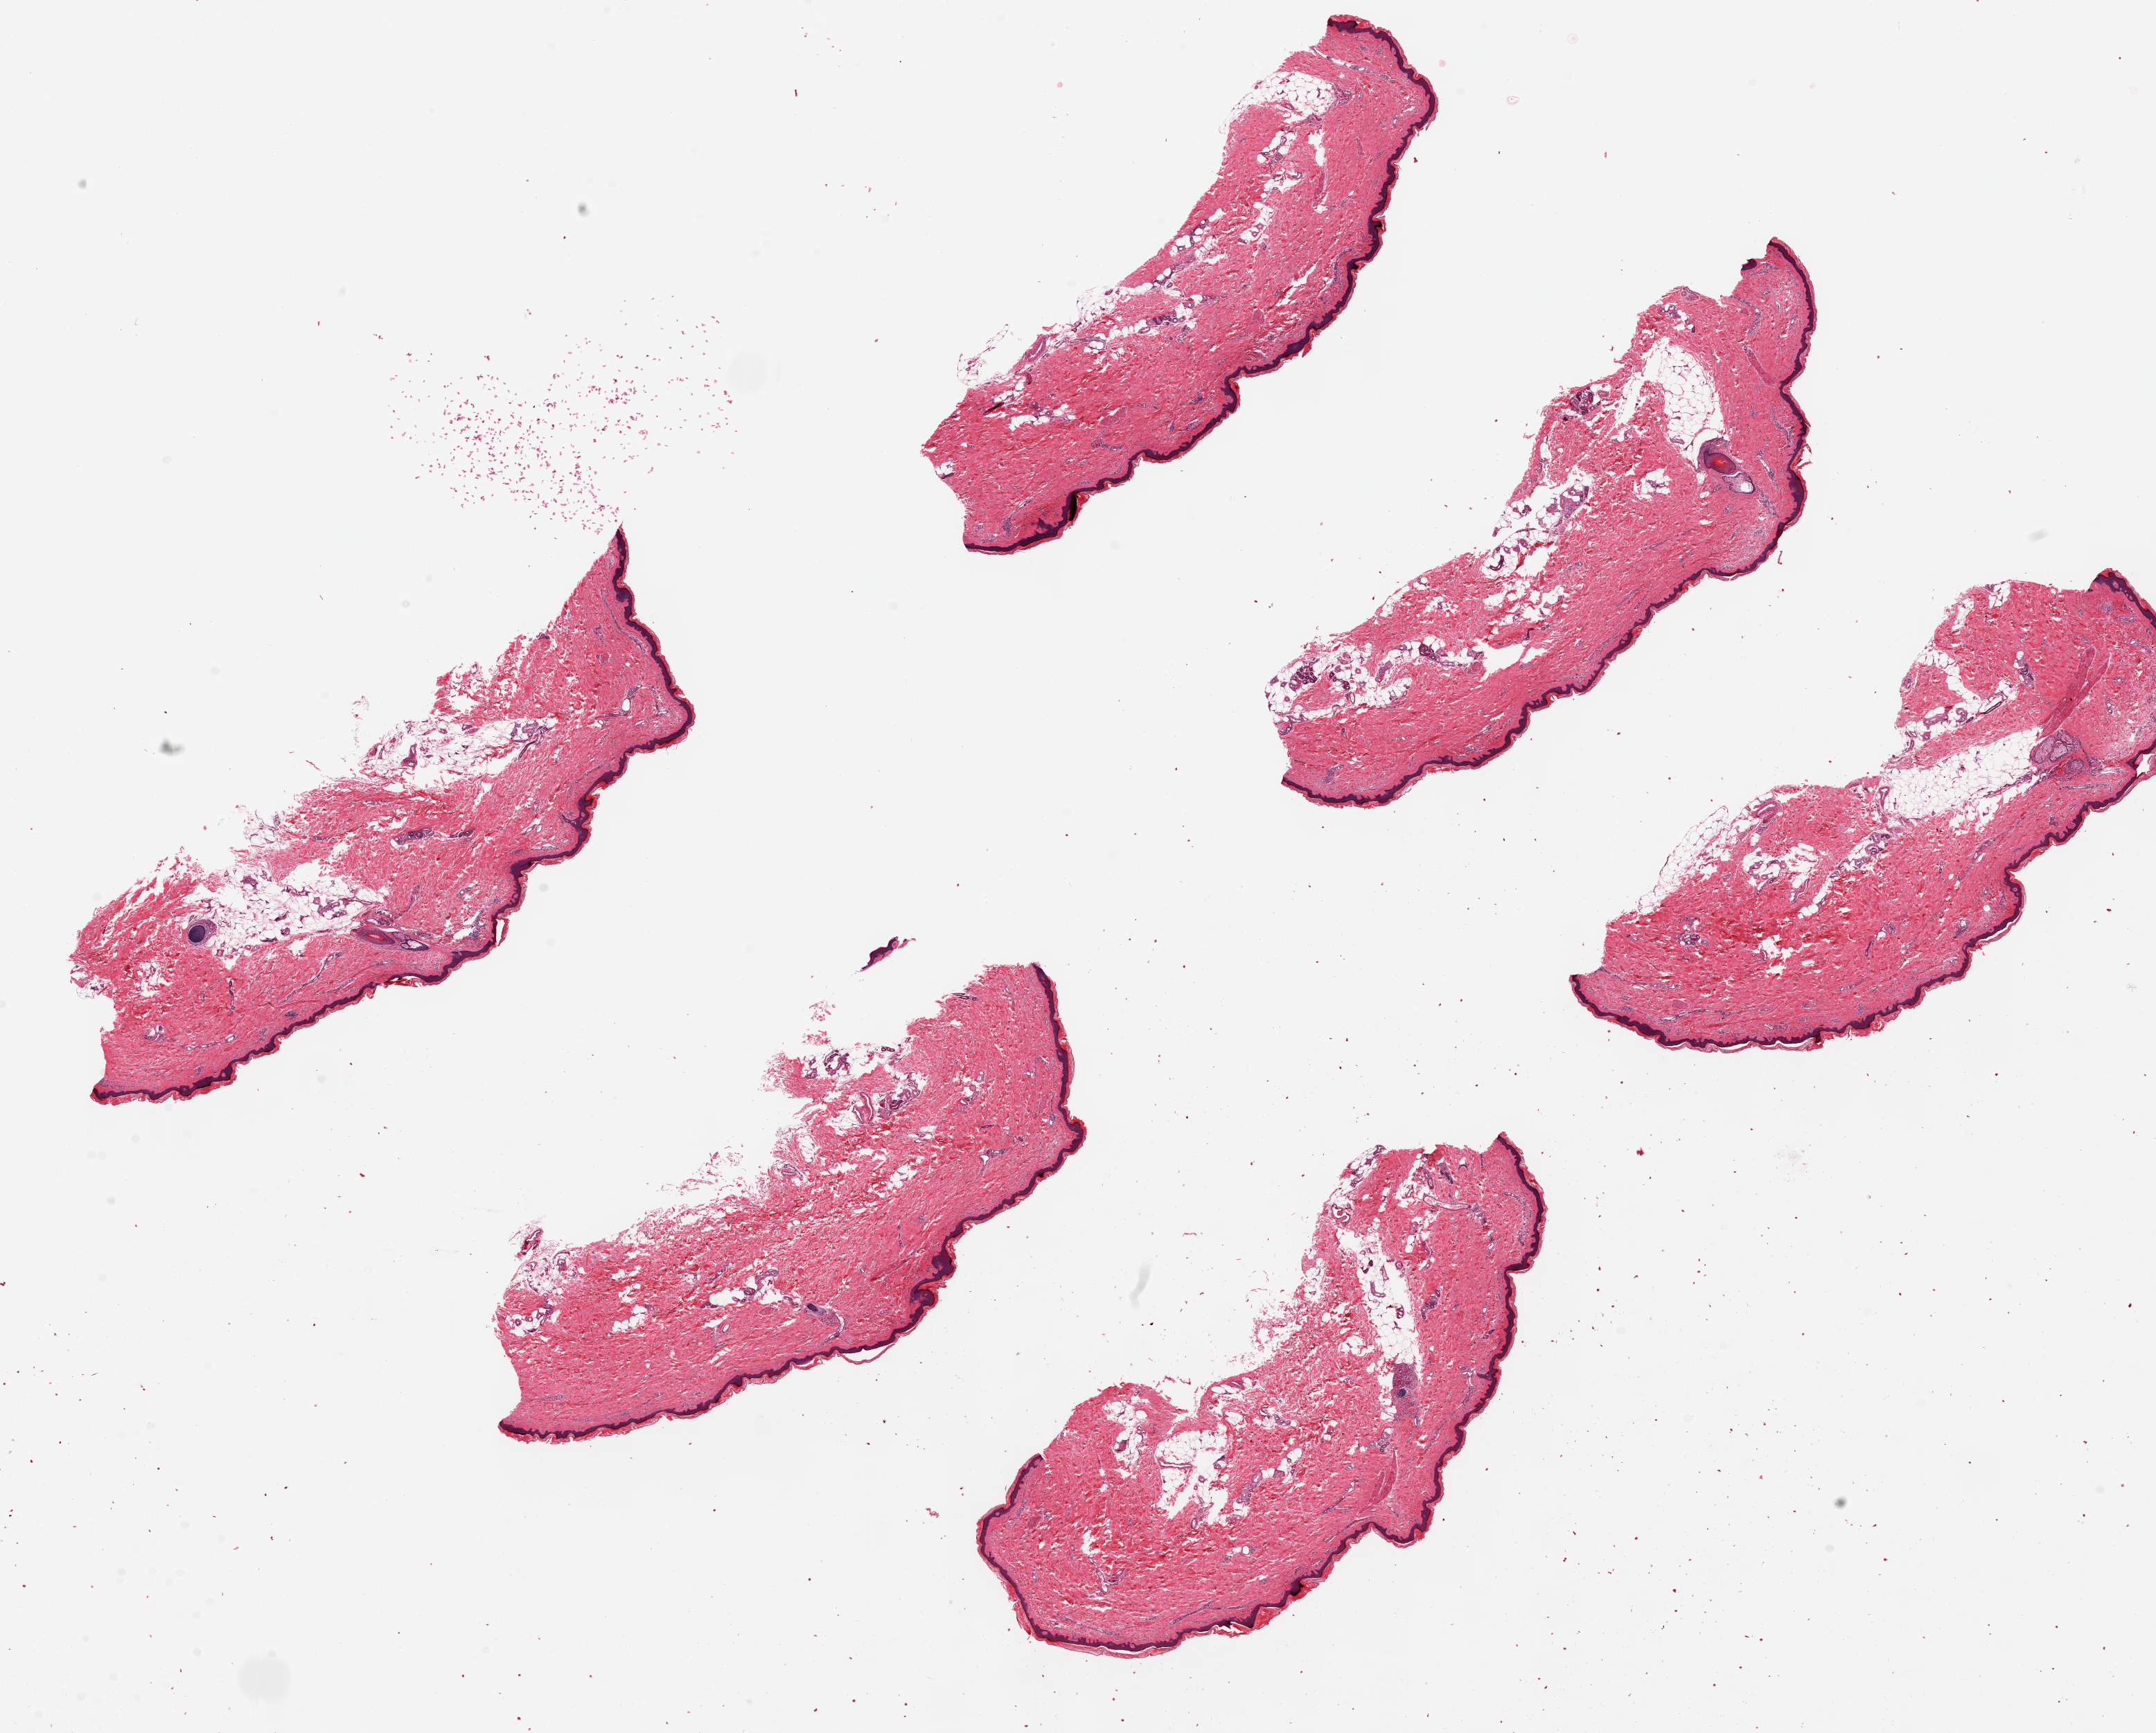
Digitized hematoxylin and eosin (H&E)-stained section, brightfield — a low-resolution overview of the entire scanned area, about 24.6 x 19.8 mm, PAXgene-fixed paraffin-embedded (PFPE) section, target tissue: skin of lower leg, donor tissue sample. Female donor.
Reviewer comment on this tissue sample: 6 ~8x2.5mm pieces. Squamous epithelium is ~1--2% of thickness.